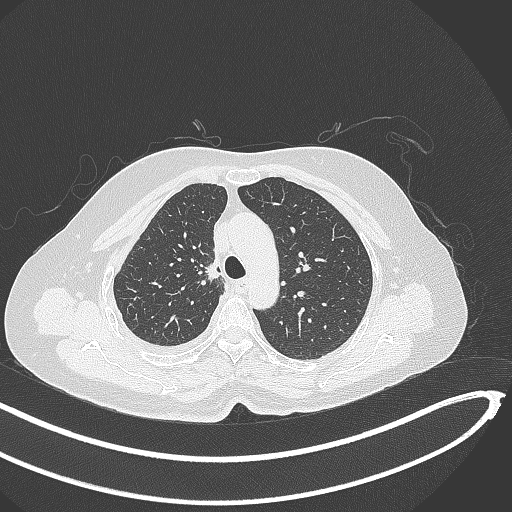
Chest CT, one axial slice. Position 276 of 345 along the scan axis. Reconstruction kernel B70f. Lung window (W 1500 / L -600 HU). 512 × 512 image matrix, field of view 400 × 400 mm. Patient: female, 64 years. Case-level facts recorded for this patient, not image findings: clinical TNM (as recorded): T1b N0 M1.
Structures marked on this image (rectangle marked by the reading radiologist):
- lung tumour (recorded histology: adenocarcinoma): bounding box (x1, y1, x2, y2) in pixels: (201, 255, 226, 286)